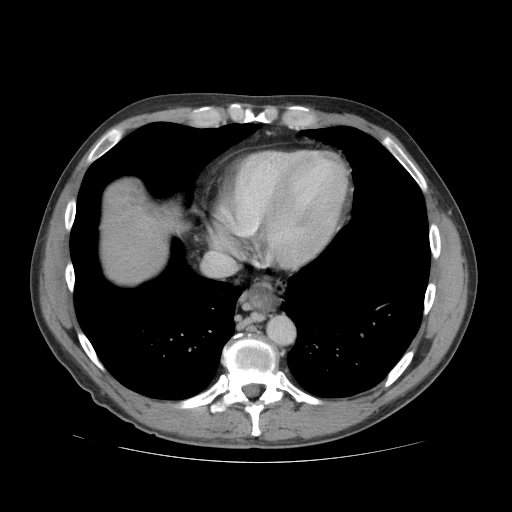
Contrast-enhanced abdominal CT (liver protocol), one axial slice. Position 72 of 81 along the scan axis. Reconstruction kernel STANDARD. 140 kVp. Soft-tissue window (W 400 / L 40 HU). 2.5 mm slice thickness. 512 × 512 image matrix, field of view 400 × 400 mm. From the clinical record (not read from this slice): diagnosis: hepatocellular carcinoma (patient treated with transarterial chemoembolisation; whether this scan precedes or follows treatment is not stated here); TNM stage (as recorded): Stage-IVB; Child-Pugh class: B; tumour differentiation: well differentiated.
Structures marked on this image (semi-automatic segmentation, software-assisted and operator-edited):
- liver parenchyma outside the tumour (the mass and vessels are separate outlines, so this box may not span the whole liver): bounding box <101,178,178,282> (left, top, right, bottom; pixels)
- mass: <105,180,144,220>